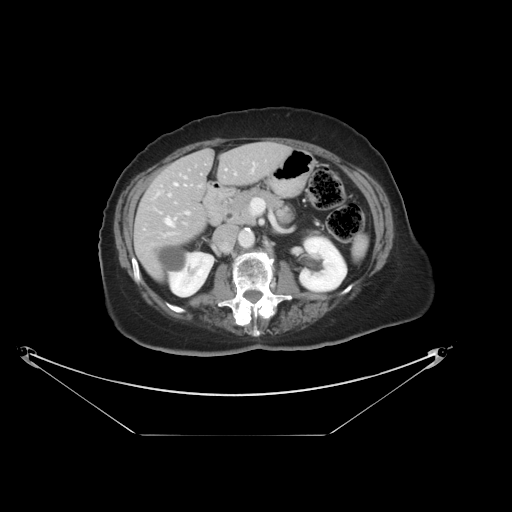
Contrast-enhanced abdominal CT, one axial slice. Slice 16 of 36 in the series (ordered by position). Reconstruction kernel STANDARD. Soft-tissue window (W 400 / L 40 HU). 5 mm slice thickness. 512 × 512 image matrix, field of view 500 × 500 mm. Female patient, age 70 years. From the clinical record (not read from this slice): diagnosis: colorectal cancer liver metastases, imaged before liver resection; multiple liver metastases: no; largest metastasis: 2.5 cm; chemotherapy before resection: no.
Structures marked on this image (expert manual segmentation):
- hepatic veins: bounding box <165,169,227,226> (left, top, right, bottom; pixels)
- liver: <136,143,289,278>
- planned liver remnant (the part of the liver to remain after resection): <136,143,289,278>
- portal vein (with intrahepatic branches): <160,173,237,215>